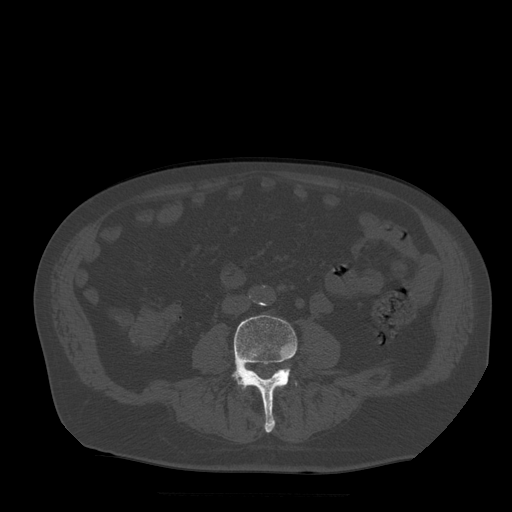
CT including the spine, one axial slice; position 114 of 522 along the scan axis; bone window (W 1800 / L 400 HU); 1.25 mm slice thickness; 512 × 512 image matrix, field of view 420 × 420 mm. Patient age 72 years. Case-level facts recorded for this patient, not image findings: primary cancer: prostate.
Structures marked on this image (semi-automatic segmentation, software-assisted and operator-edited):
- L3 vertebra: bounding box (x1, y1, x2, y2) in pixels: (246, 385, 280, 389)
- L4 vertebra: (231, 315, 297, 433)
- L5 vertebra: (238, 367, 291, 388)